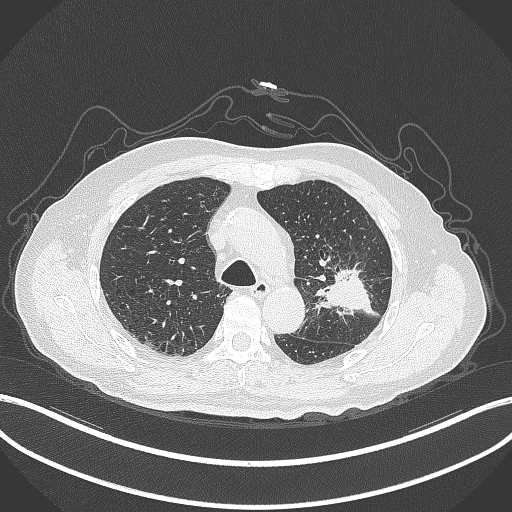
Chest CT, one axial slice. Position 205 of 331 along the scan axis. Lung window (W 1500 / L -600 HU). 512 × 512 image matrix. Male patient, age 79 years. Case-level facts recorded for this patient, not image findings: clinical TNM (as recorded): T2a N1 M1; histopathological grade: G3.
Annotated regions visible in this slice (bounding box drawn by a radiologist):
- lung tumour (recorded histology: adenocarcinoma): bounding box <310,261,378,318> (left, top, right, bottom; pixels)